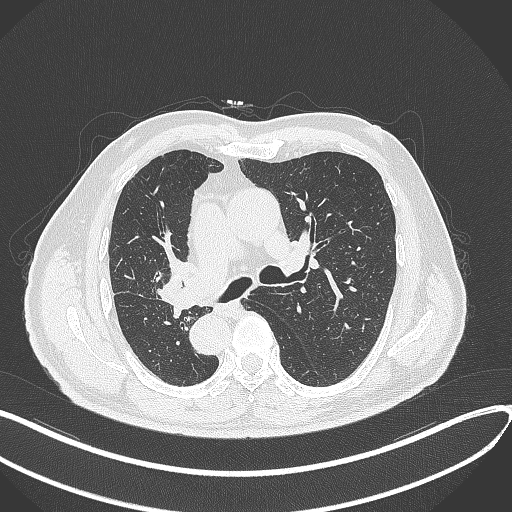
Chest CT, one axial slice. Position 181 of 300 along the scan axis. Reconstruction kernel B70f. 120 kVp. Lung window (W 1500 / L -600 HU). 512 × 512 image matrix, field of view 400 × 400 mm. Male patient, age 67 years. From the clinical record (not read from this slice): clinical TNM (as recorded): T2a N0 M0.
Annotated regions visible in this slice (bounding box drawn by a radiologist):
- lung tumour (recorded histology: squamous cell carcinoma): bounding box <152,257,186,300> (left, top, right, bottom; pixels)